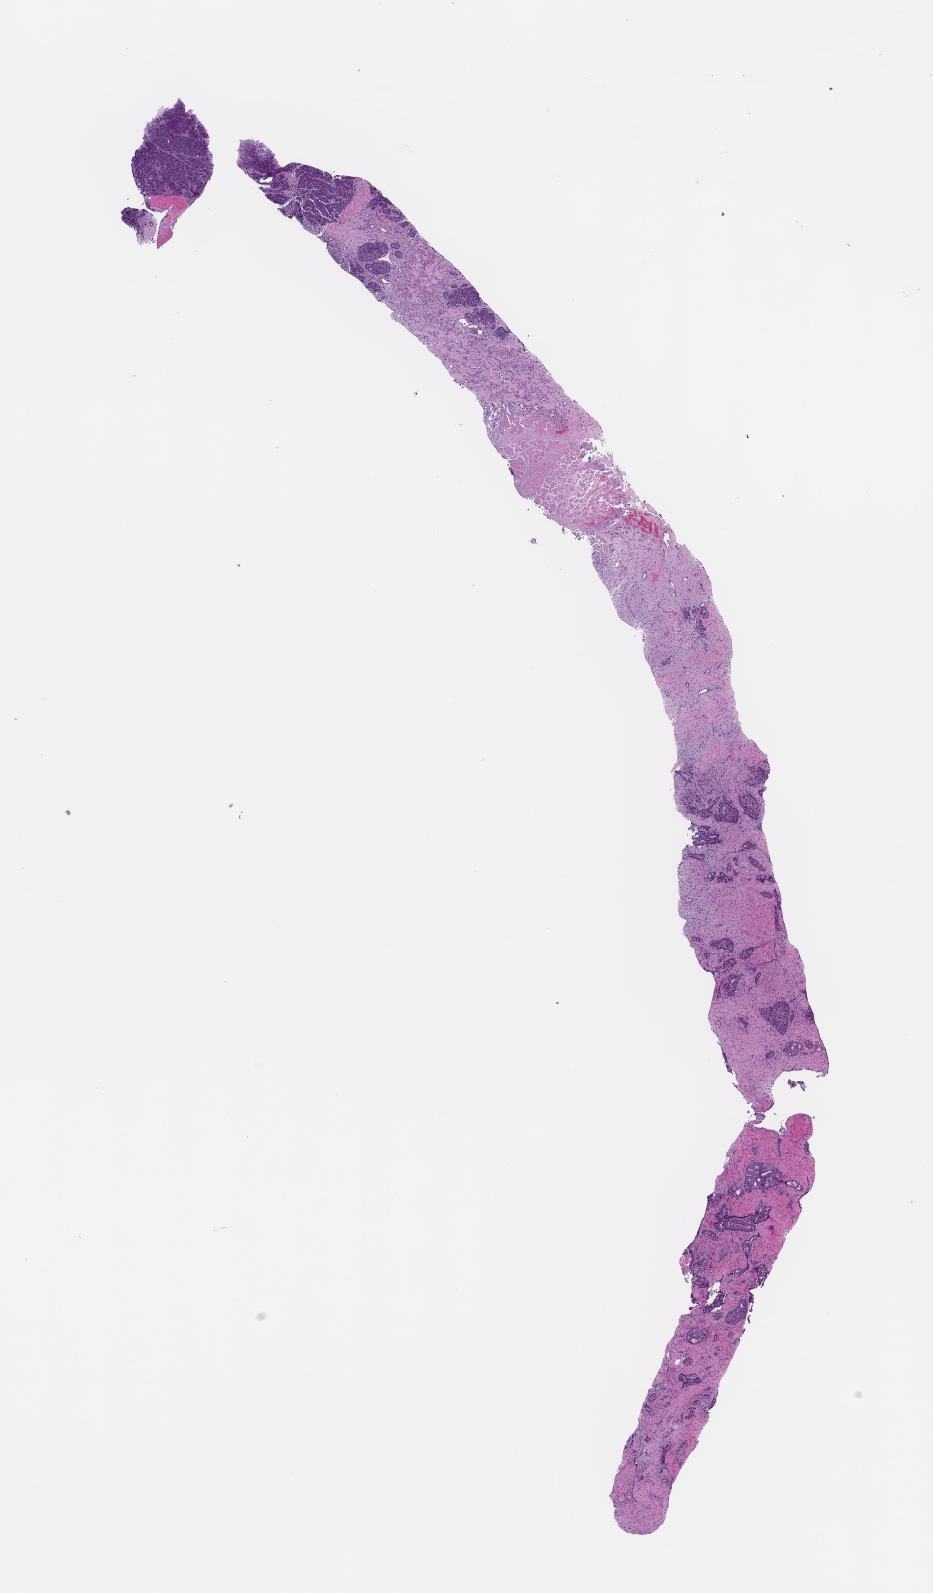
Digitized hematoxylin and eosin (H&E)-stained section — low-resolution overview of the scanned area, about 7.5 x 12.9 mm; formalin-fixed, paraffin-embedded (FFPE) tissue; tissue site: prostate; specimen time point: archival tissue. Patient sex: male.
This section: primary tumour tissue. Diagnosis: Prostate Carcinoma.